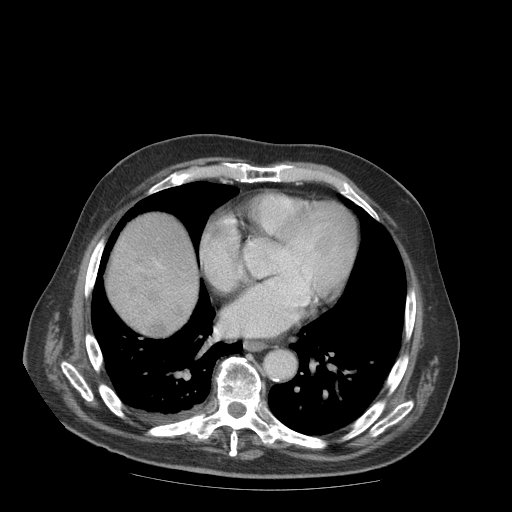
Contrast-enhanced abdominal CT (liver protocol), one axial slice. Position 91 of 99 along the scan axis. 140 kVp. Soft-tissue window (W 400 / L 40 HU). 2.5 mm slice thickness. 512 × 512 image matrix, field of view 420 × 420 mm. From the clinical record (not read from this slice): diagnosis: hepatocellular carcinoma (patient treated with transarterial chemoembolisation; whether this scan precedes or follows treatment is not stated here); TNM stage (as recorded): Stage-IIIB; Child-Pugh class: A; tumour differentiation: well differentiated; tumour nodularity: multinodular.
Structures marked on this image (semi-automatic segmentation, software-assisted and operator-edited):
- abdominal aorta: bounding box [x1, y1, x2, y2] px = [265, 349, 295, 378]
- liver parenchyma outside the tumour (the mass and vessels are separate outlines, so this box may not span the whole liver): [106, 212, 198, 334]
- liver vessels: [156, 262, 160, 266]